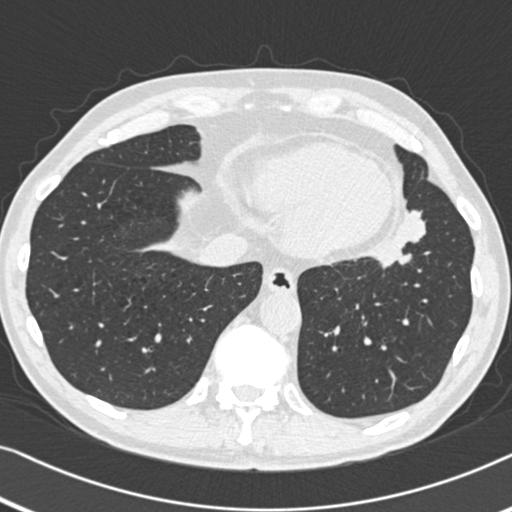
Low-dose screening chest CT, one axial slice. Position 128 of 383 along the scan axis. Lung window (W 1500 / L -600 HU). 512 × 512 image matrix, field of view 332 × 332 mm.
Outlined on this slice (manually delineated by an expert):
- lesion 1 (tumor, upper lobe of left lung): box from (x=376, y=210) to (x=426, y=267) px